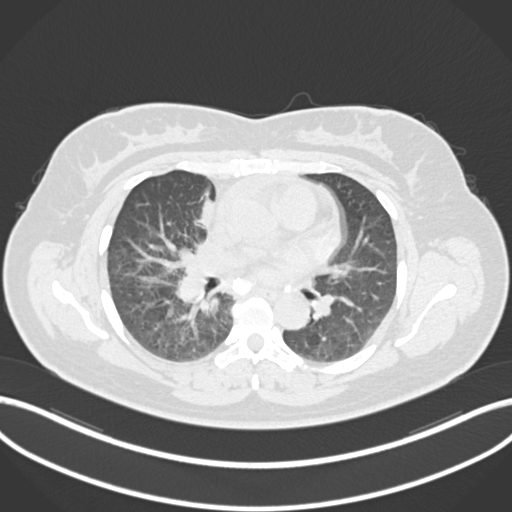
Chest CT, one axial slice. Position 89 of 183 along the scan axis. 120 kVp. Lung window (W 1500 / L -600 HU). 1 mm slice thickness. 512 × 512 image matrix, field of view 400 × 400 mm. Female patient, age 46 years. From the clinical record (not read from this slice): clinical TNM (as recorded): T2a N1 M0.
Annotated regions visible in this slice (bounding box drawn by a radiologist):
- lung tumour (recorded histology: adenocarcinoma): bounding box <189,201,222,231> (left, top, right, bottom; pixels)